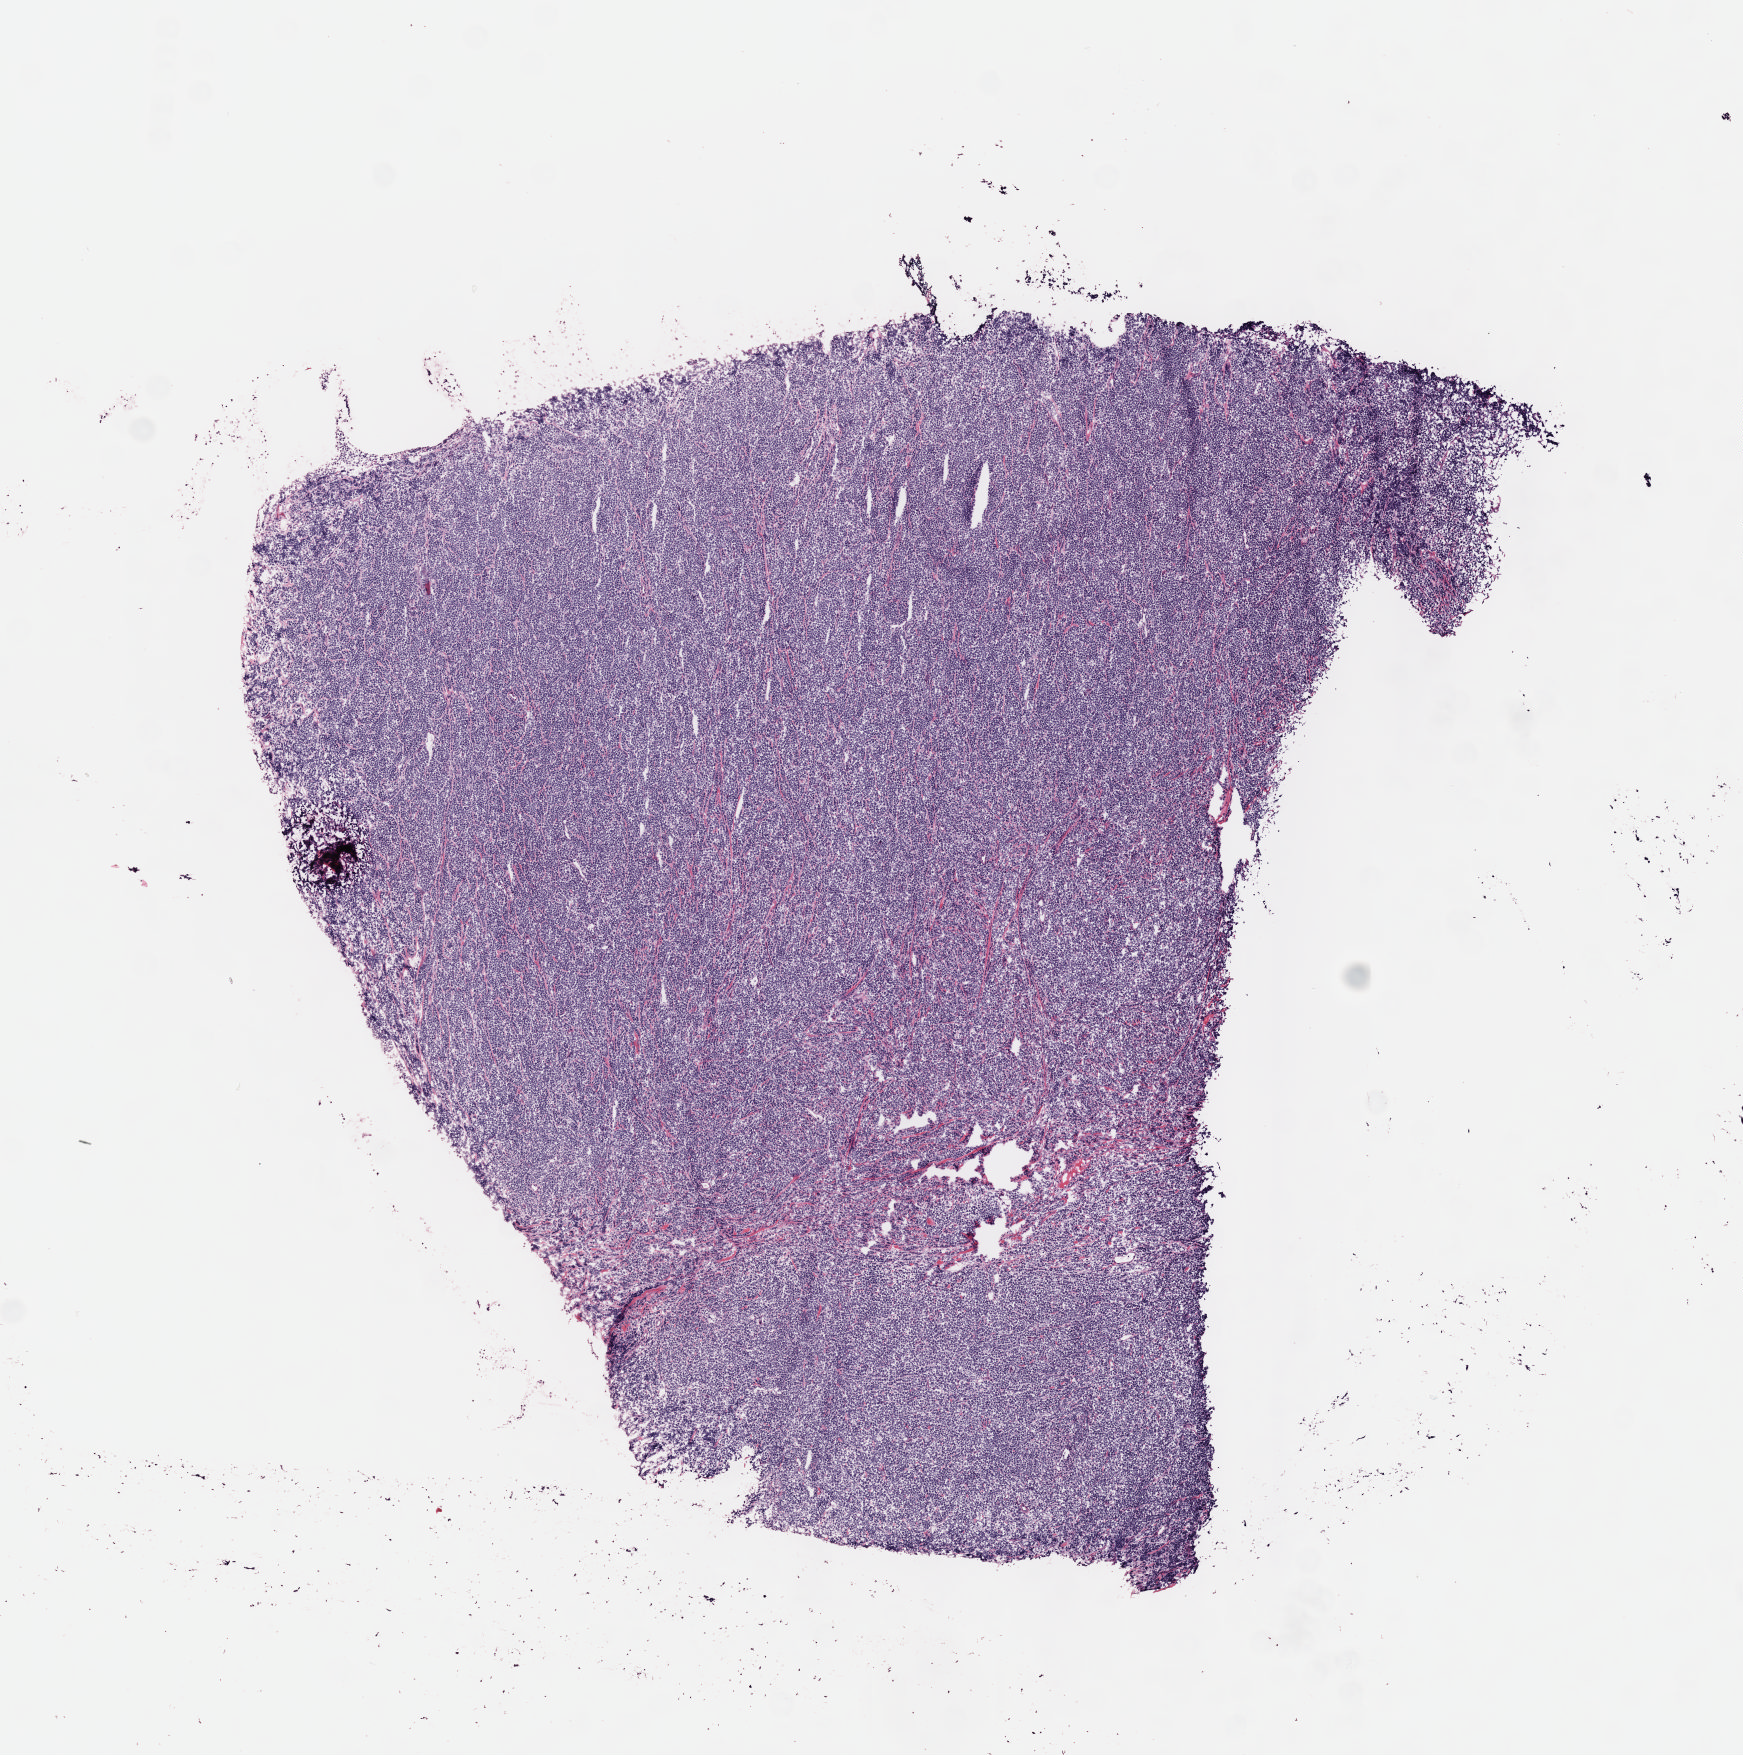
Digitized hematoxylin and eosin (H&E)-stained section, shown as a low-resolution overview of the whole scanned area (about 7.0 x 7.1 mm); frozen section; primary tumor; anatomic site: cranium. Male patient; age at initial diagnosis 5 years. Composition of this section per pathologist review: tumor cells 95%, tumor nuclei 95%, stromal cells 5%, necrosis 0%, normal cells 0%. Infiltration values recorded for this section: lymphocyte infiltration 45%, monocyte infiltration 30%, neutrophil infiltration 5%.
* section: top of the tissue portion
* Ann Arbor stage (patient): Stage II
* histologic diagnosis: Burkitt lymphoma, NOS